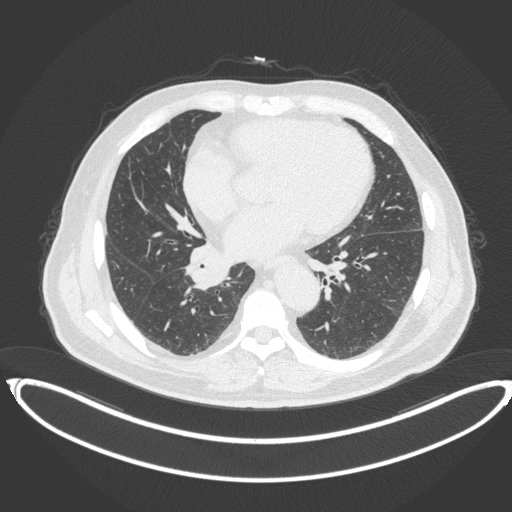
Chest CT, one axial slice. Position 180 of 383 along the scan axis. Reconstruction kernel B31f. Lung window (W 1500 / L -600 HU). 1 mm slice thickness. 512 × 512 image matrix, field of view 448 × 448 mm. Male patient, age 61 years. From the clinical record (not read from this slice): clinical TNM (as recorded): T1b N1 M0.
Structures marked on this image (bounding box drawn by a radiologist):
- lung tumour (recorded histology: squamous cell carcinoma): bounding box (x1, y1, x2, y2) in pixels: (181, 246, 230, 291)